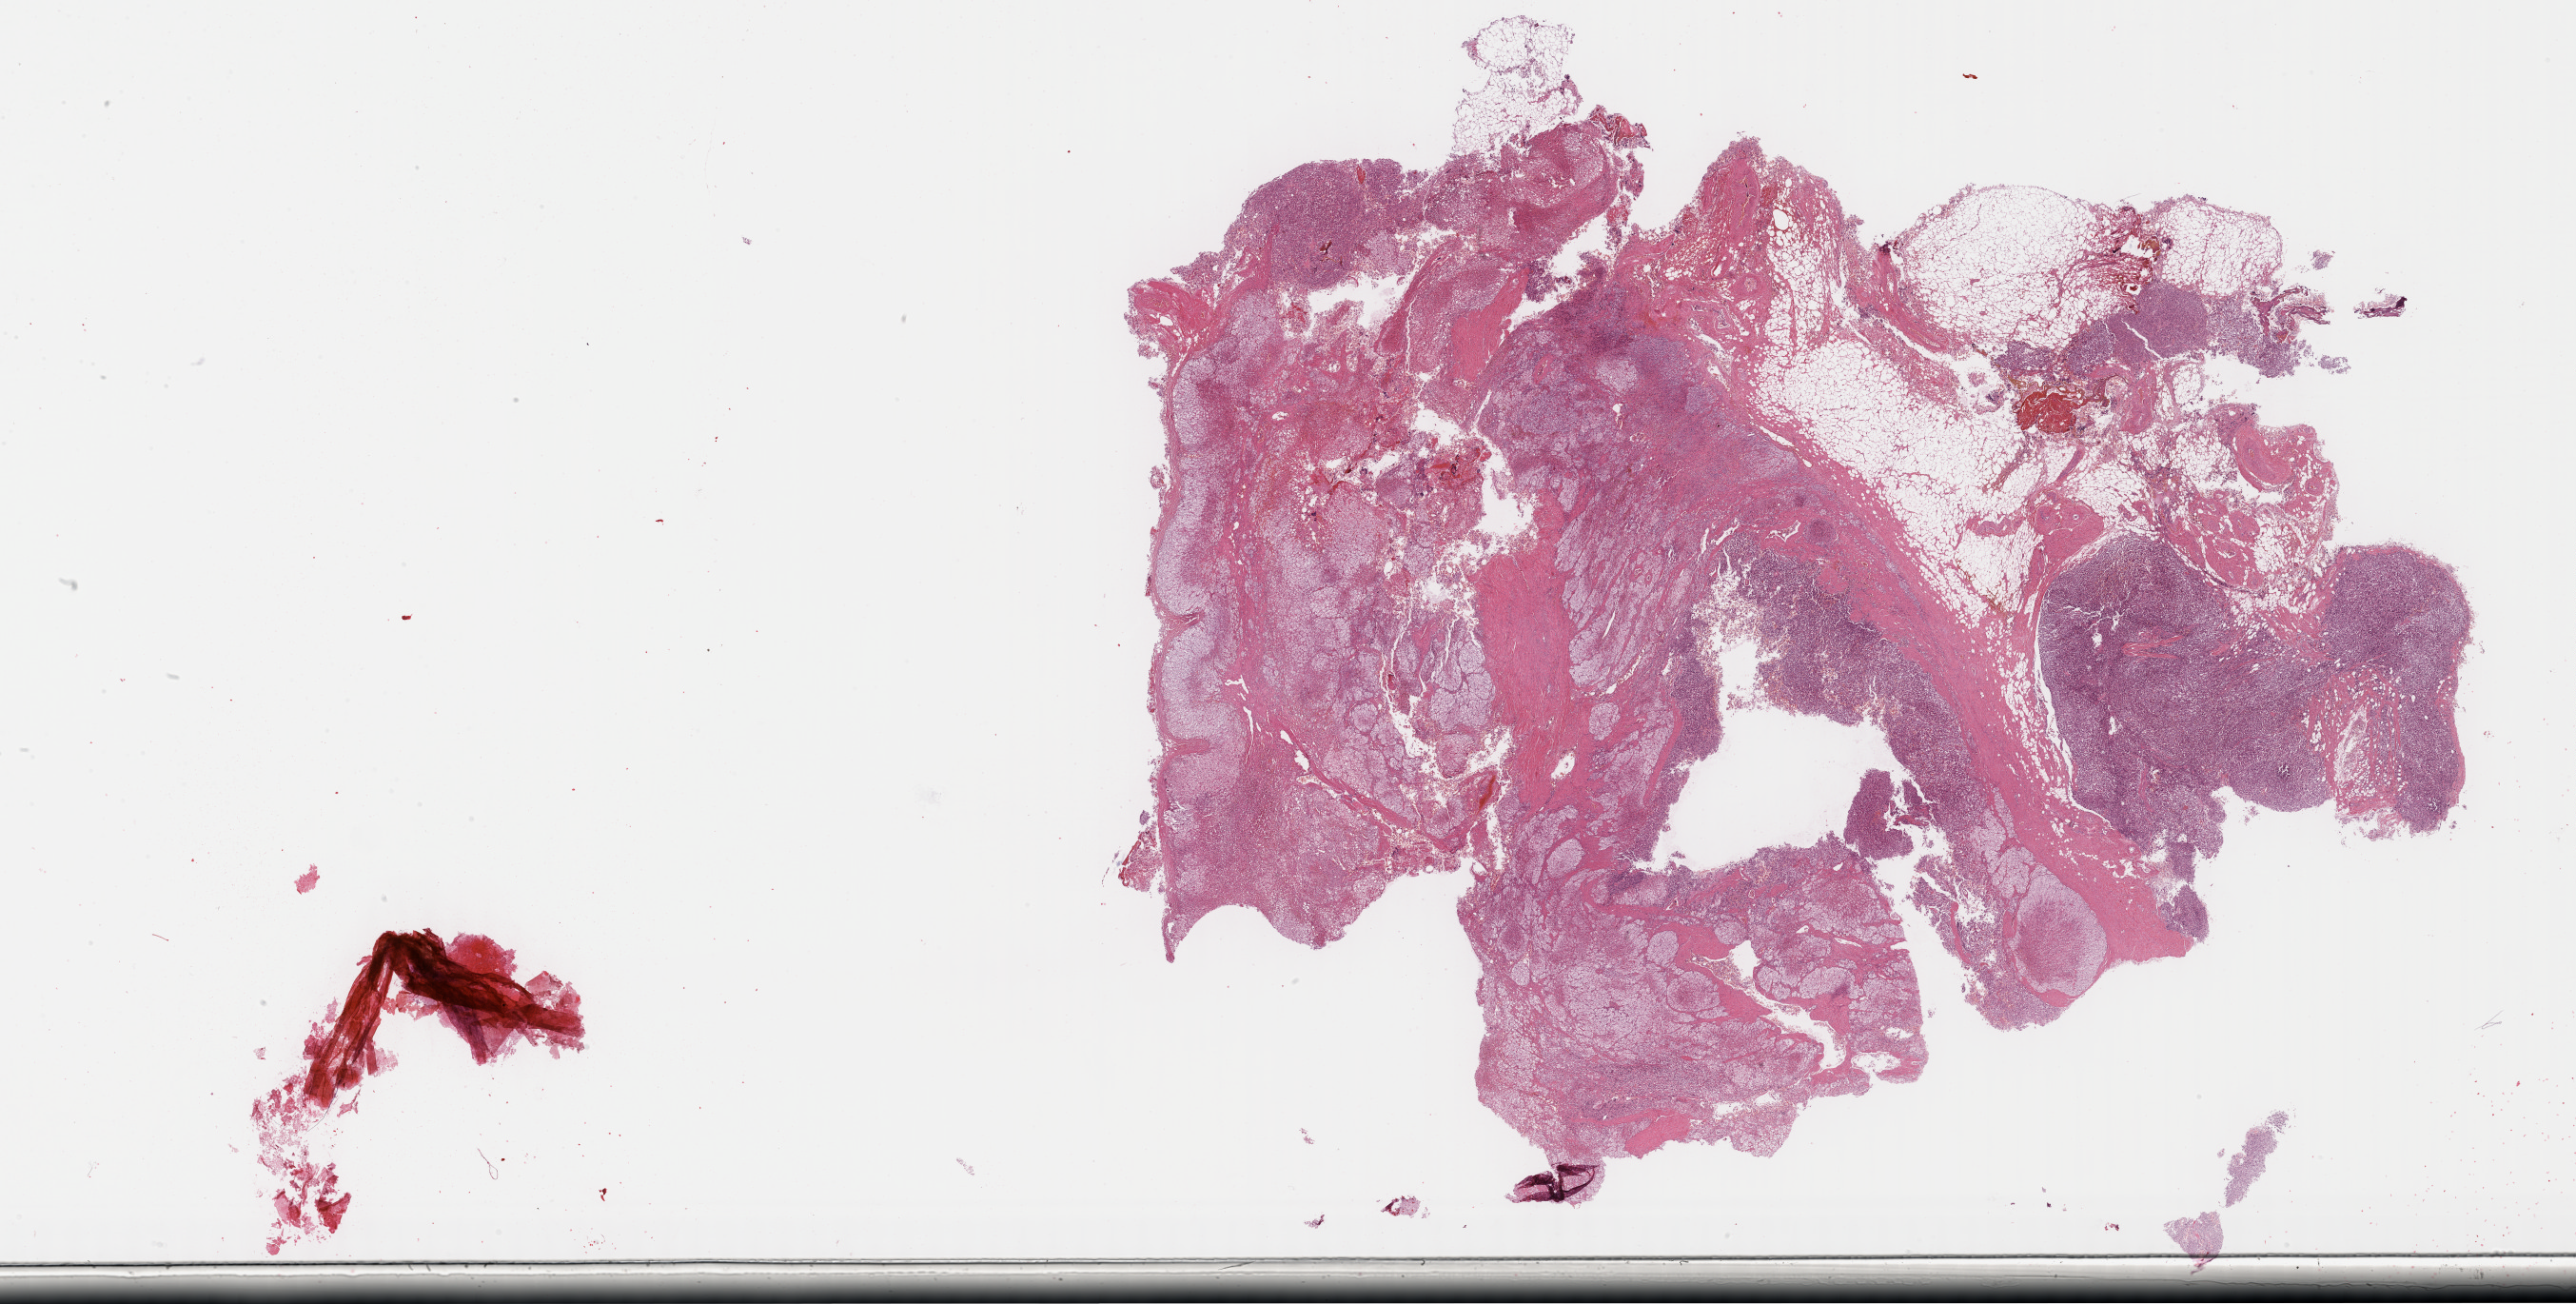
H&E whole-slide image, low-resolution overview of the scanned area, about 43.8 x 22.2 mm (slide scanned at 40x), formalin-fixed paraffin-embedded (FFPE) diagnostic section, primary tumour sample from the adrenal gland. Patient: male, age at initial diagnosis 74 years.
Diagnosis: Pheochromocytoma, malignant.